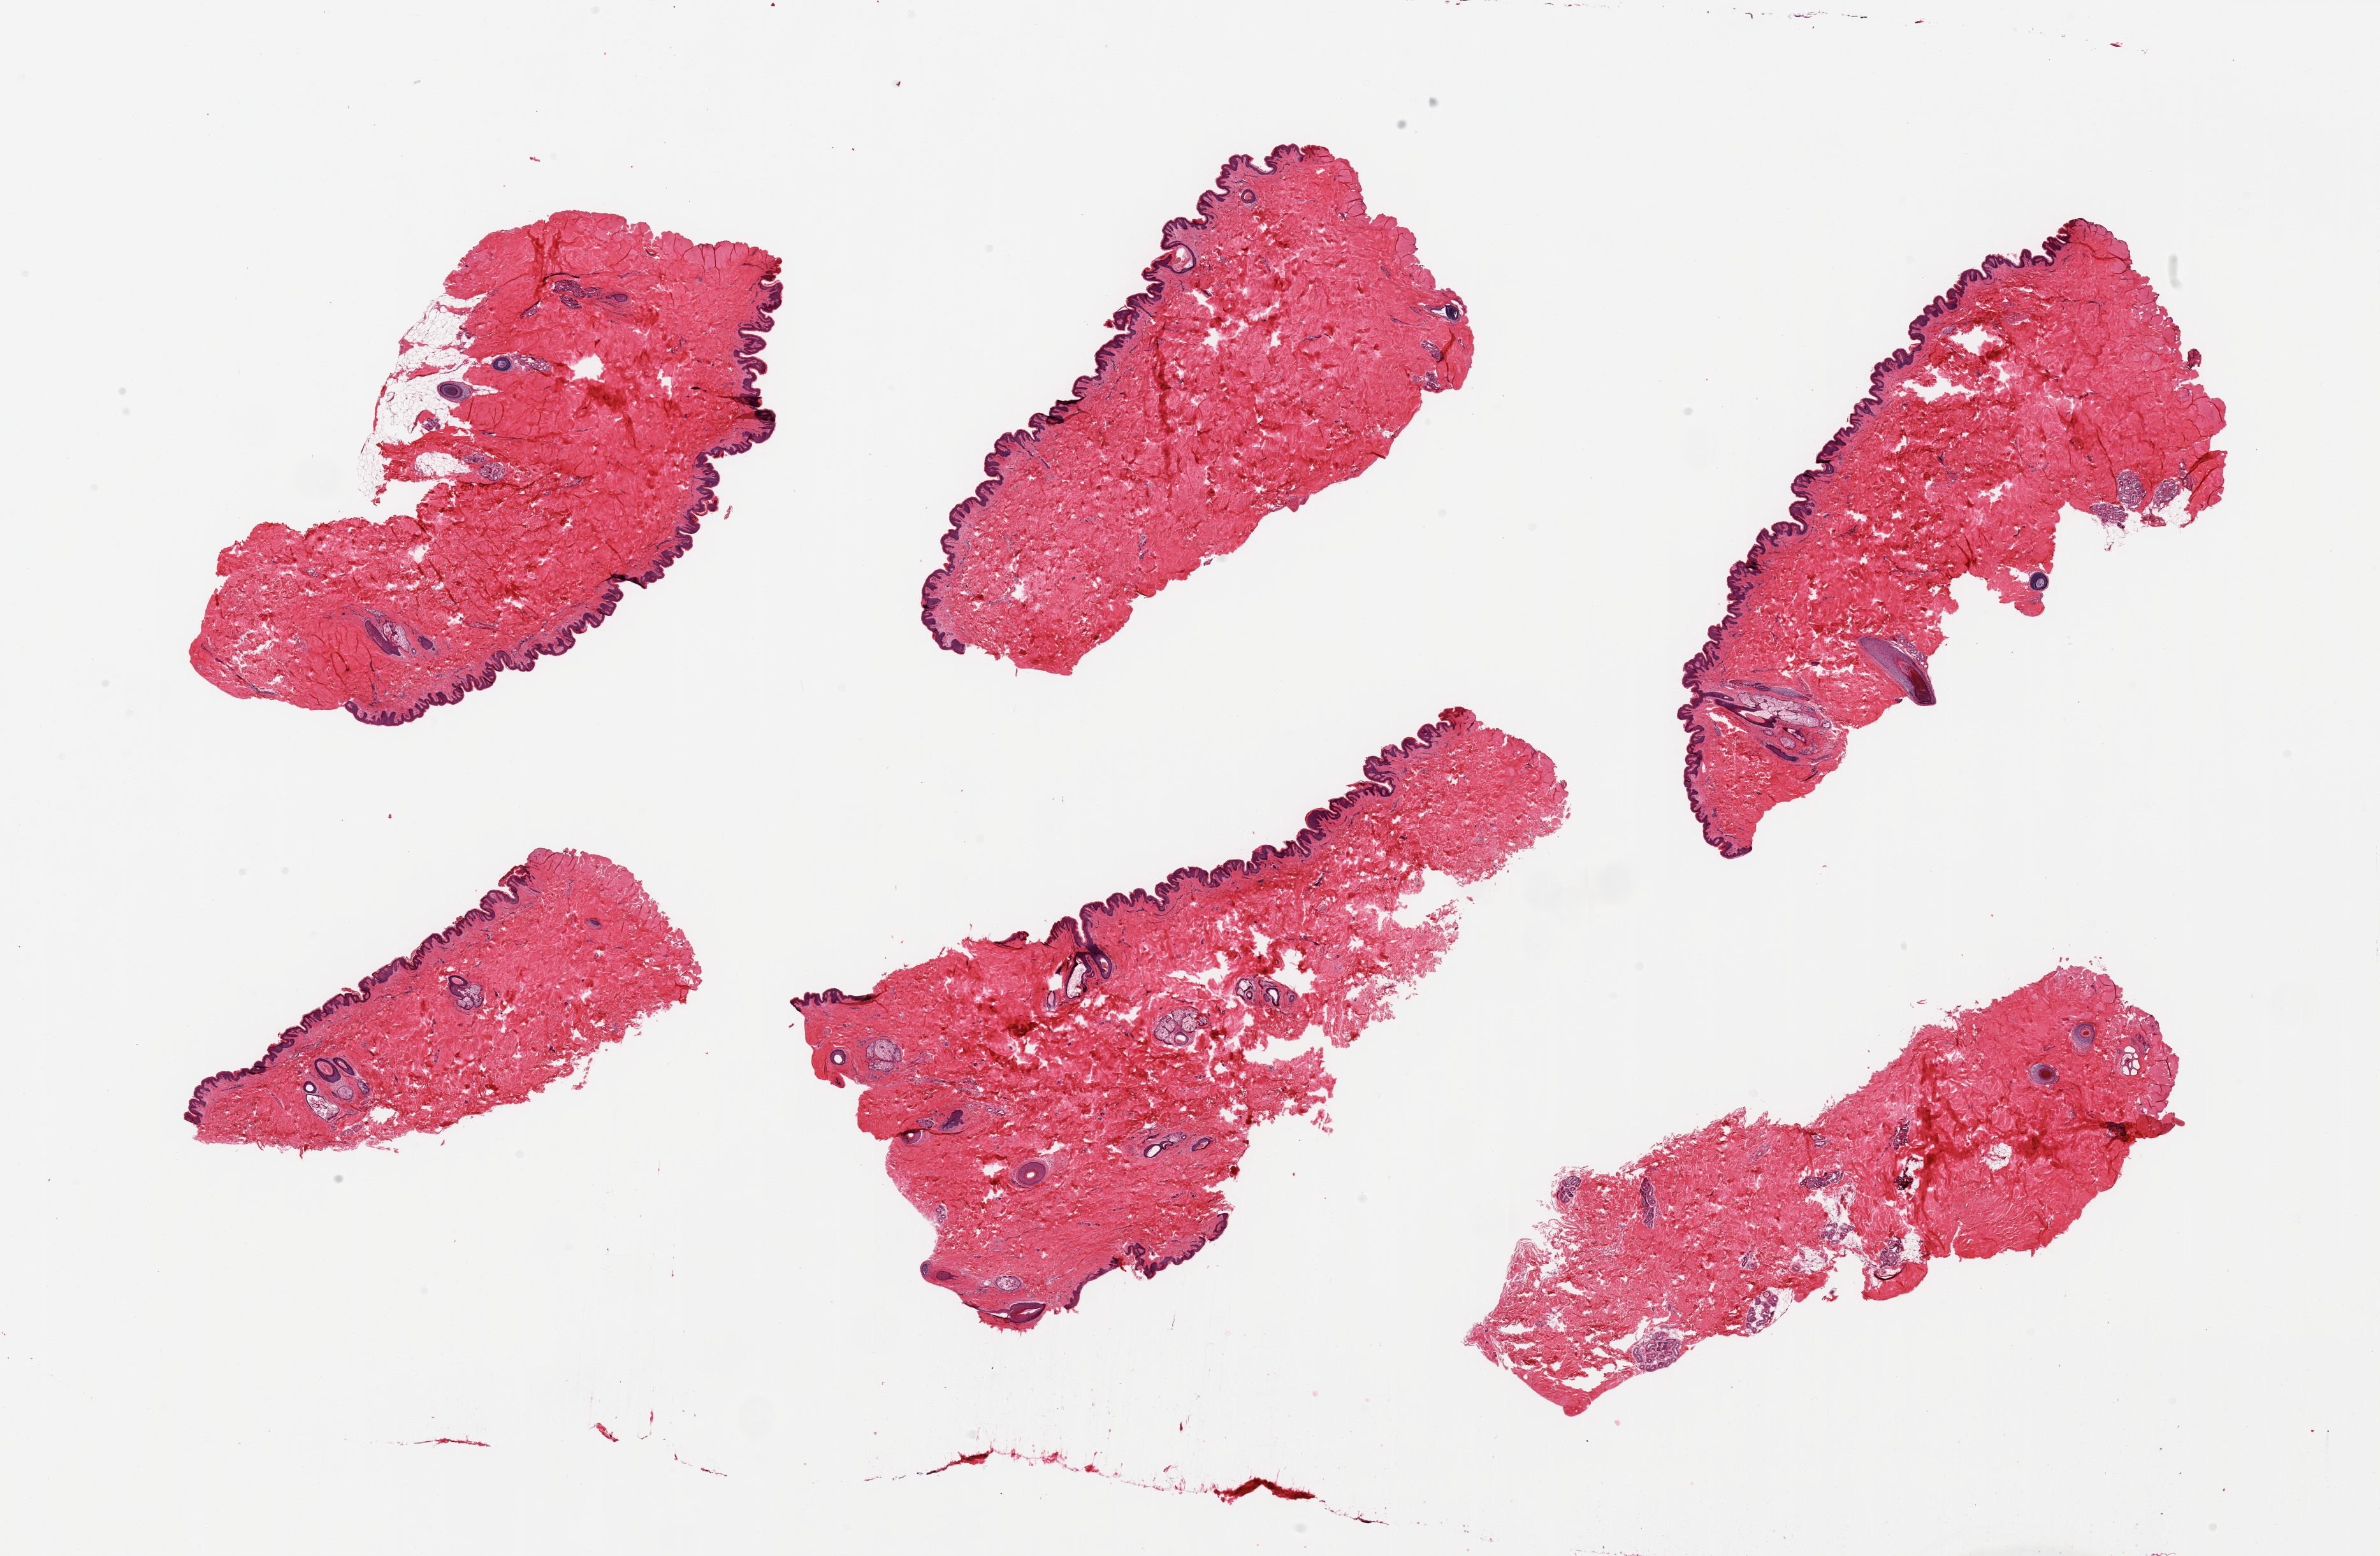
Digitized H&E-stained section, brightfield, low-resolution overview of the scanned area, about 29.5 x 19.3 mm, PAXgene-fixed paraffin-embedded (PFPE) section, target tissue: skin of suprapubic region, donor tissue sample. Donor sex: male.
Reviewer comment on this tissue sample: 6 pieces; several pieces have hair follicles with prominent sebaceous glands; 5/6 well trimmed; 1 without epidermis.